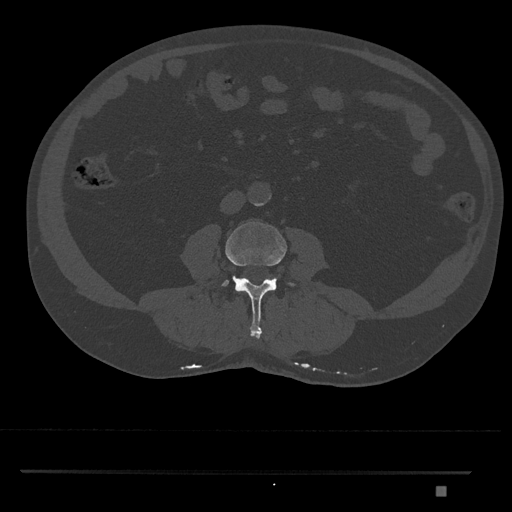
CT including the spine, one axial slice. Position 673 of 1134 along the scan axis. 120 kVp. Bone window (W 1800 / L 400 HU). 0.5 mm slice thickness. 512 × 512 image matrix, field of view 429 × 429 mm. Male patient, age 65 years. Case-level facts recorded for this patient, not image findings: primary cancer: prostate.
Annotated regions visible in this slice (semi-automatic segmentation, software-assisted and operator-edited):
- L3 vertebra: bounding box <222,222,295,339> (left, top, right, bottom; pixels)